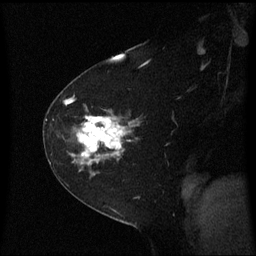
Breast MRI (dynamic contrast-enhanced), one sagittal slice. Position 42 of 60 along the scan axis. Dynamic contrast-enhanced series, image 2 of 3 at this slice position (ordered by acquisition). 1.5 T. TE 4.2 ms, TR 8.4 ms. 2 mm slice thickness. 256 × 256 image matrix, field of view 210 × 210 mm. Female patient, age 60 years. Case-level facts recorded for this patient, not image findings: setting: breast cancer imaged before/during neoadjuvant chemotherapy; receptor status: triple-negative.
Structures marked on this image (semi-automatically segmented with operator editing):
- analysis volume of interest (the breast-tissue region the enhancement analysis was run in; not a lesion): bounding box (x1, y1, x2, y2) in pixels: (45, 99, 144, 182)
- tumour enhancement mask (voxels above the 70 % enhancement threshold inside the analysis volume of interest): (65, 99, 134, 166)